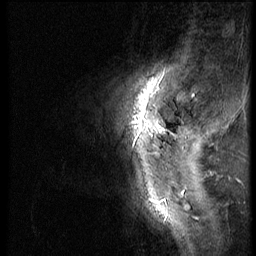
Breast MRI (dynamic contrast-enhanced), one sagittal slice; position 11 of 56 along the scan axis; dynamic contrast-enhanced series, image 2 of 3 at this slice position (ordered by acquisition); 1.5 T; TE 4.2 ms, TR 9 ms; 2.5 mm slice thickness; 256 × 256 image matrix. Patient: female, 46 years. From the clinical record (not read from this slice): setting: breast cancer imaged before/during neoadjuvant chemotherapy; receptor status: HER2-positive.
Structures marked on this image (semi-automatically segmented with operator editing):
- analysis volume of interest (the breast-tissue region the enhancement analysis was run in; not a lesion): bounding box <97,98,174,182> (left, top, right, bottom; pixels)
- tumour enhancement mask (voxels above the 140 % enhancement threshold inside the analysis volume of interest): <164,128,166,130>